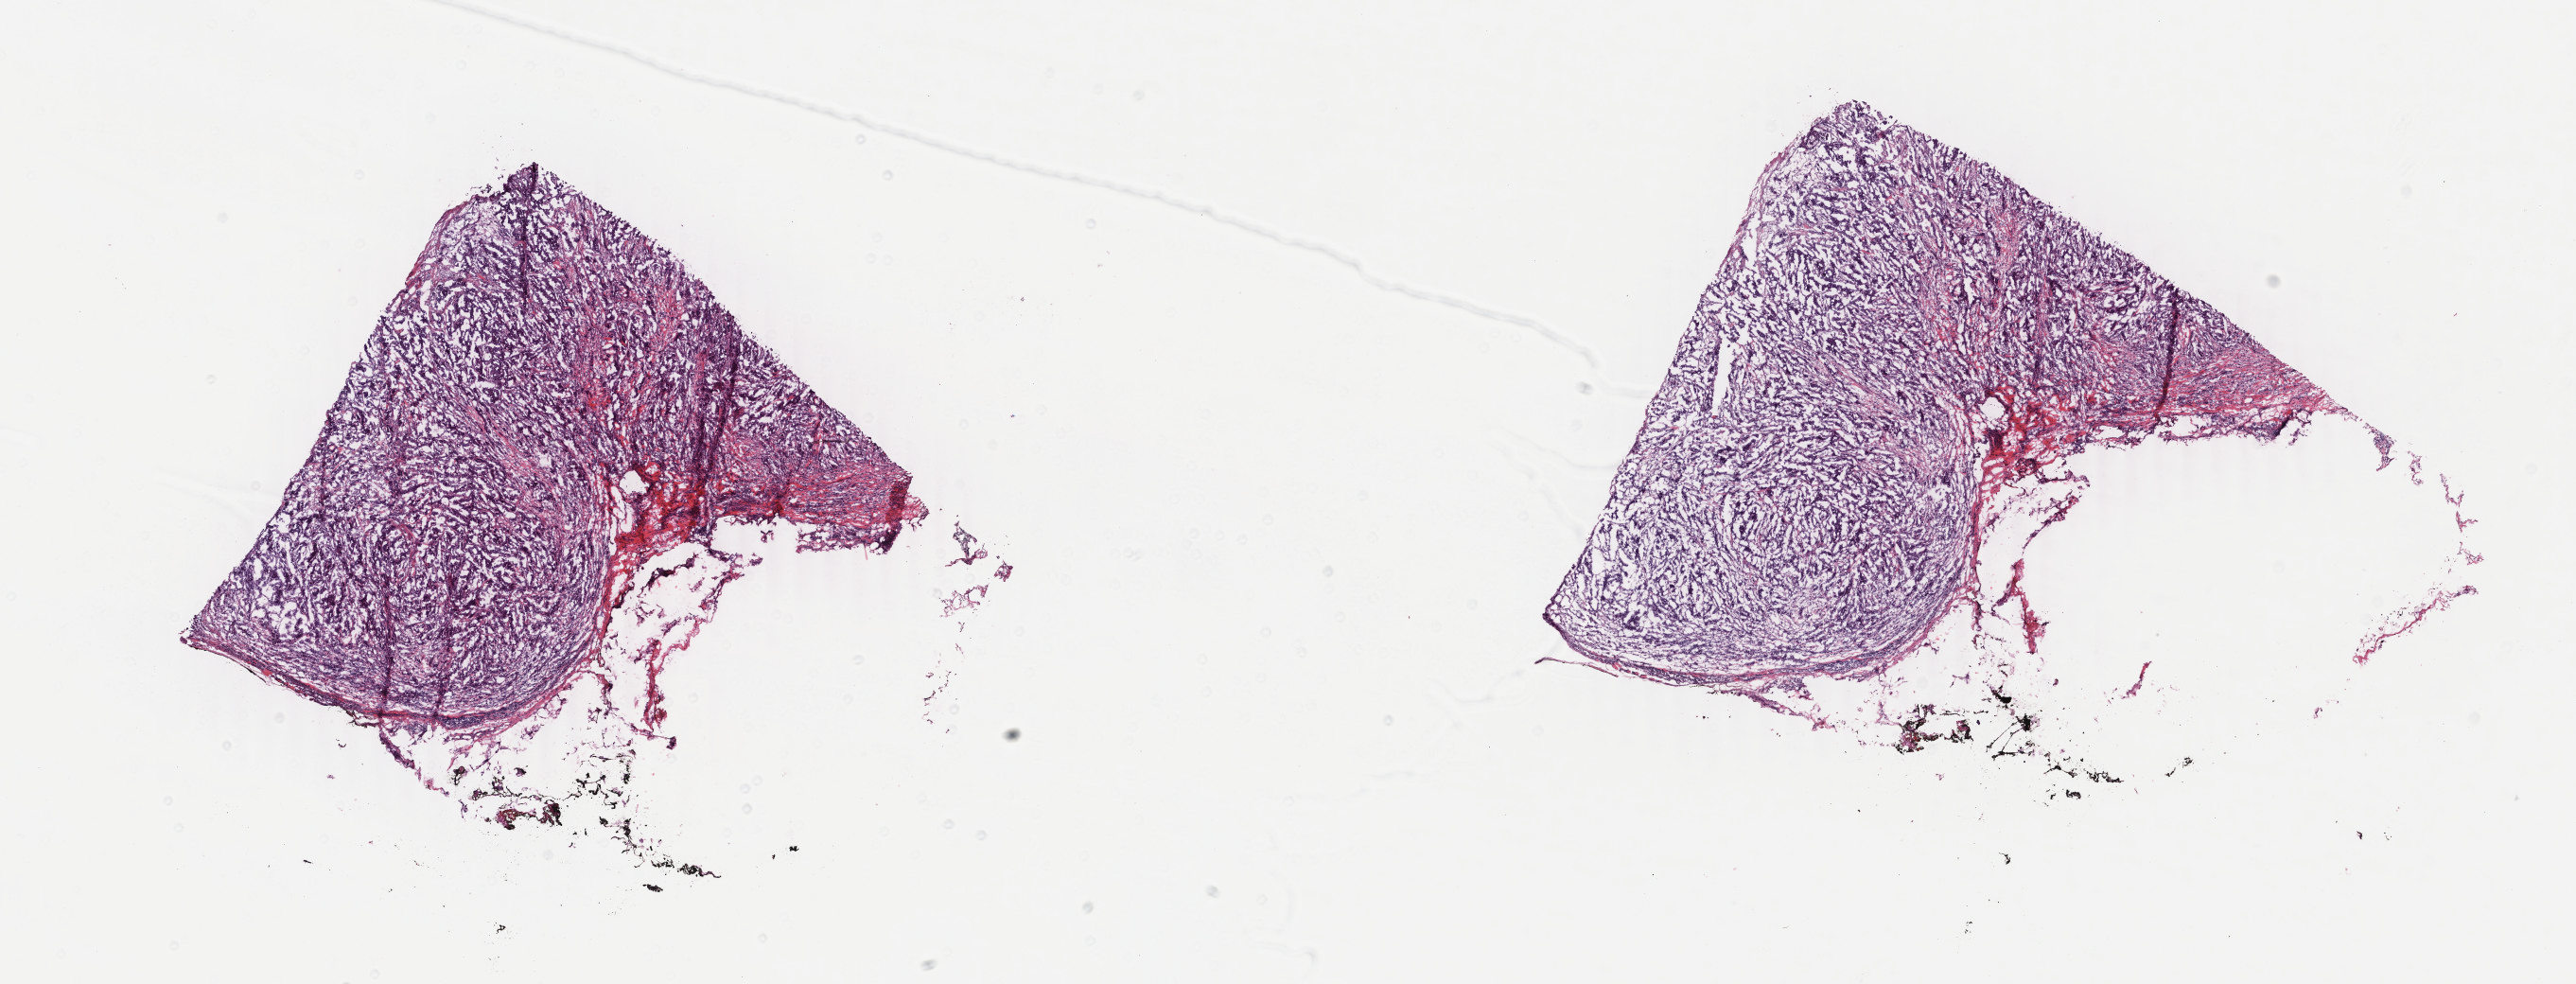
H&E whole-slide image — whole scanned area (about 21.7 x 8.3 mm, slide scanned at 40x) shown as a low-resolution overview. Frozen section. Primary tumour sample from the breast. Patient: female, age at initial diagnosis 55 years. Composition of this section per pathologist review: tumour cells 80%, tumour nuclei 80%, normal cells 0%, stromal cells 15%, necrosis 5%. Infiltration values recorded for this section: lymphocyte infiltration 30%, monocyte infiltration 10%, neutrophil infiltration 10%.
AJCC pathologic stage: IIIC. Pathologic diagnosis: Infiltrating duct carcinoma, NOS. Lymph nodes positive (case pathology): 10 of 10 examined.